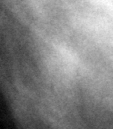
Crop from a digitized film mammogram around one marked abnormality; right breast; CC view.
- Finding: calcifications, morphology lucent center; BI-RADS assessment category 2; benign without callback (not worked up further).